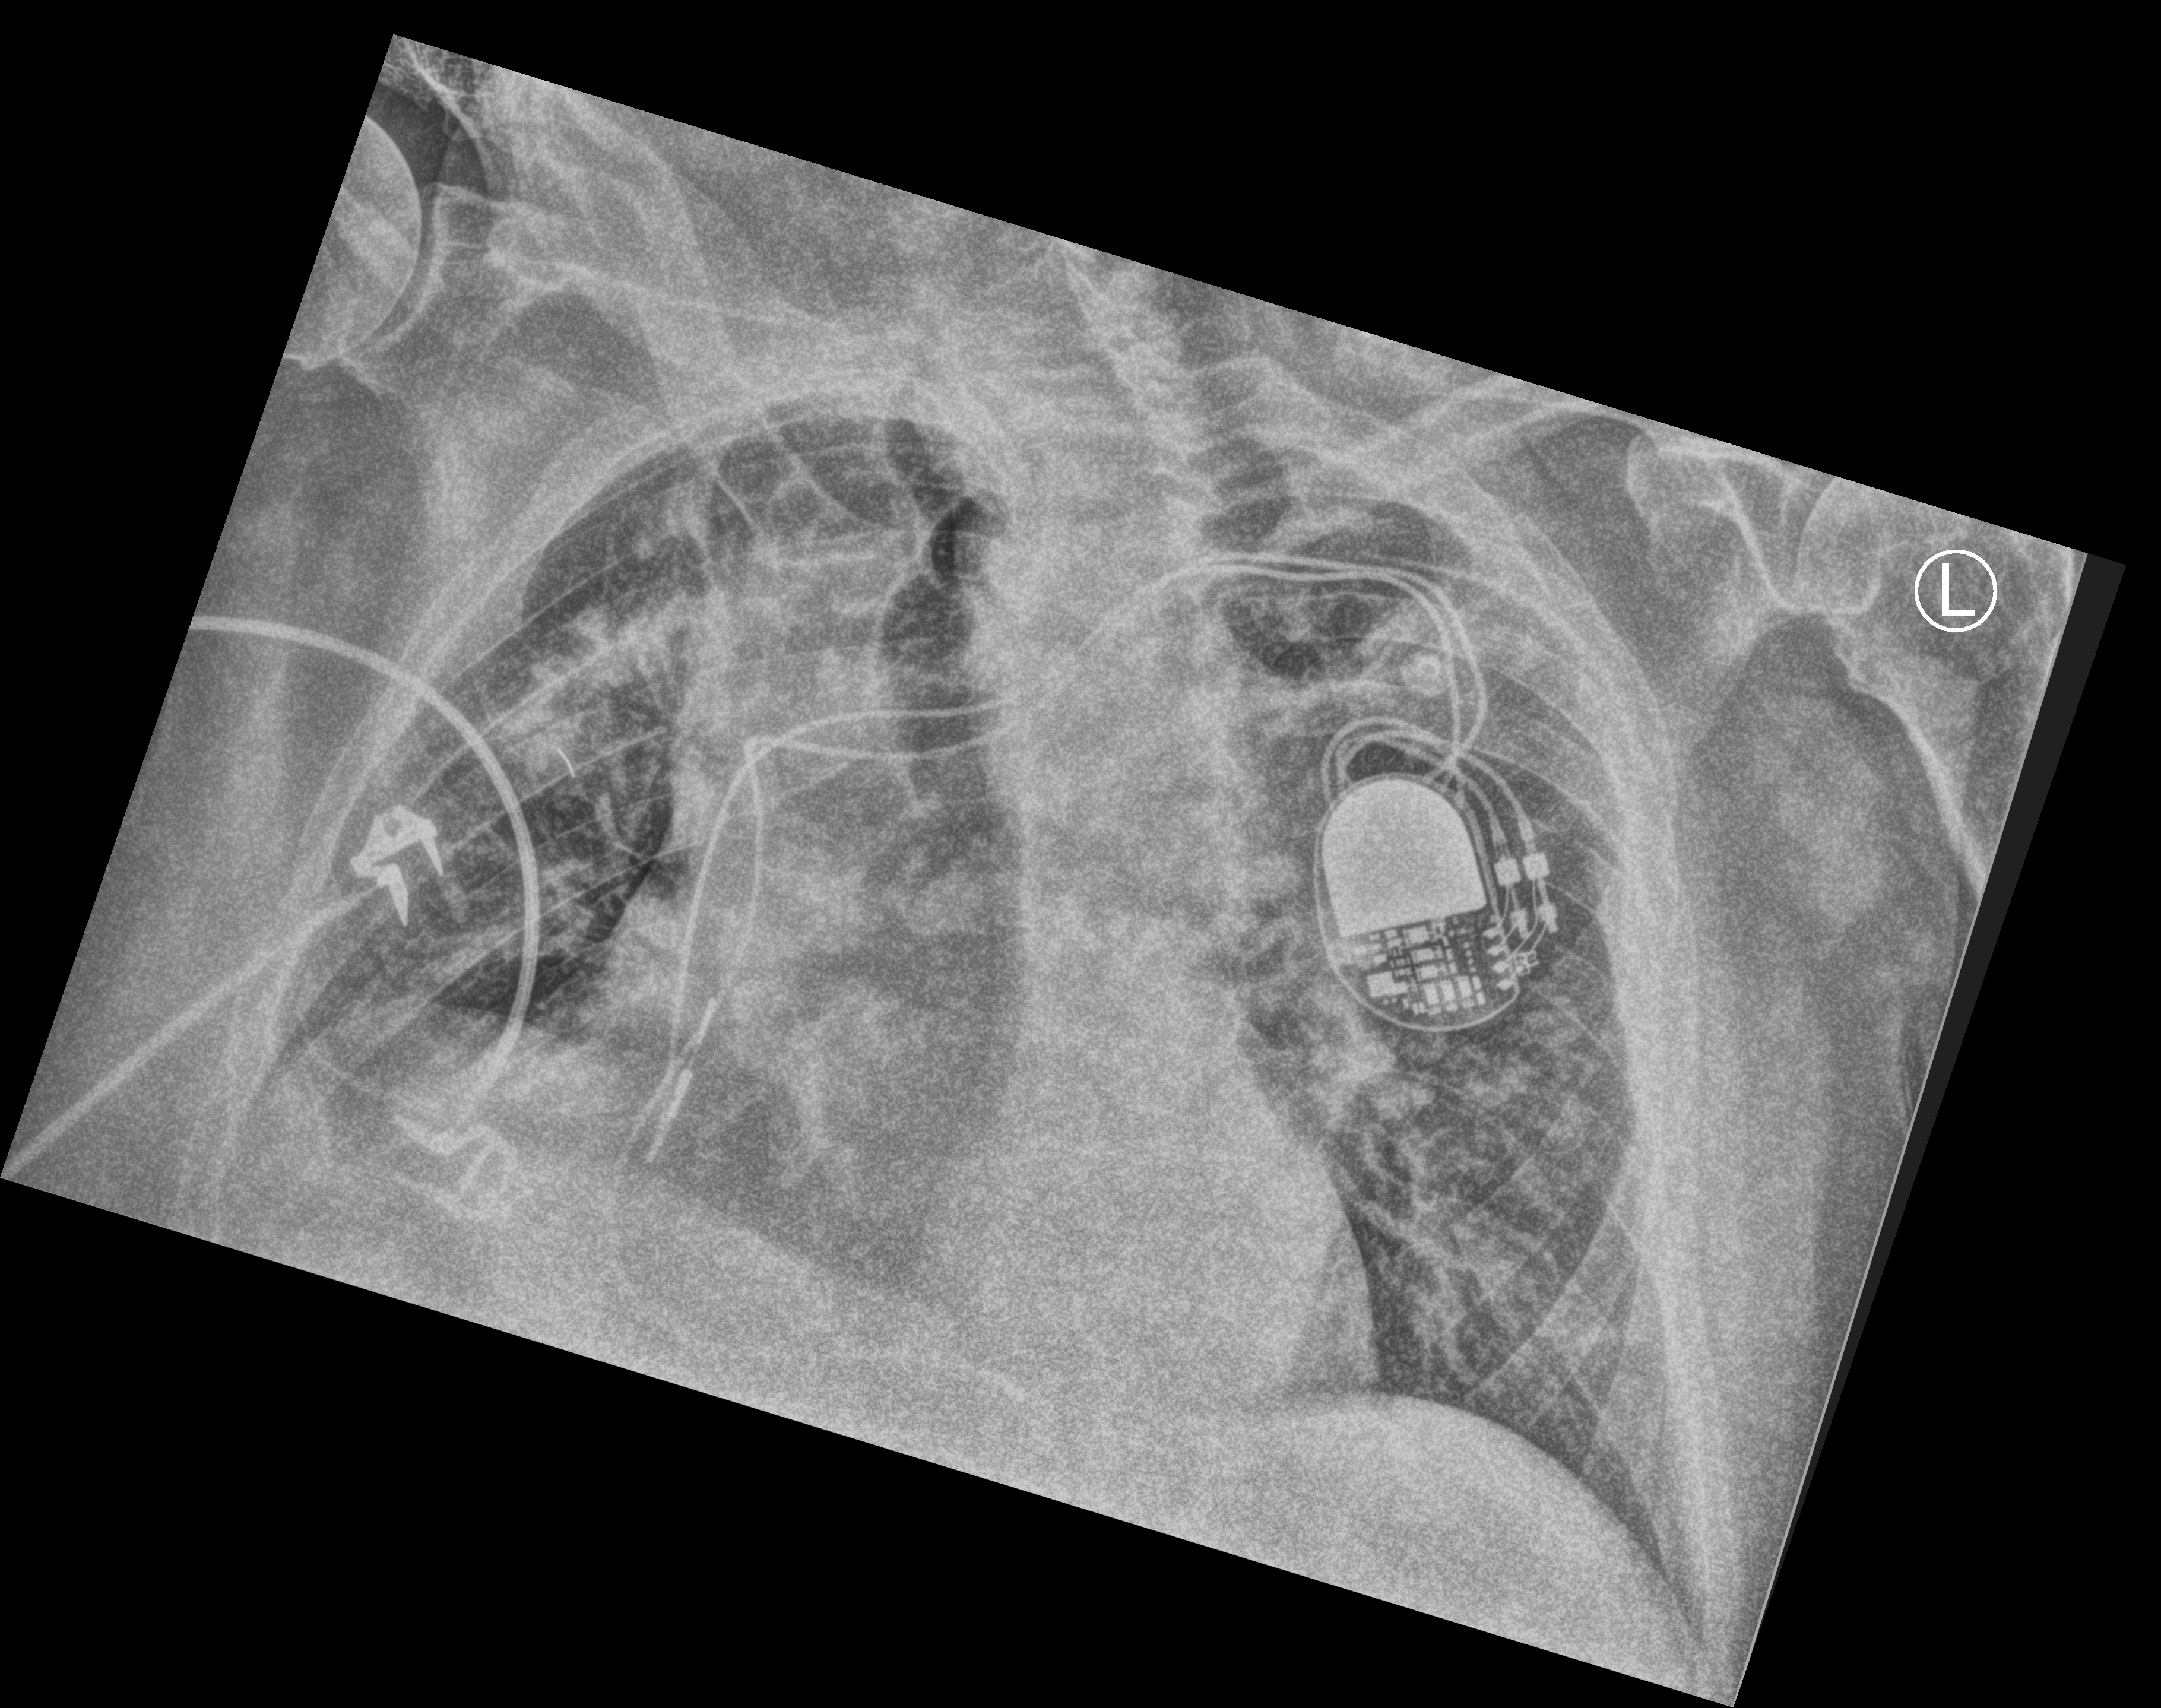
Portable chest radiograph; anteroposterior (AP) projection. Patient hospitalised with COVID-19; male, aged 75–90 years.
From the hospital-stay record, not from the radiograph (when in the stay this image was taken is not recorded):
- mechanically ventilated during this hospital stay: no
- length of hospital stay: 15 days
- hypertension (admission record): yes